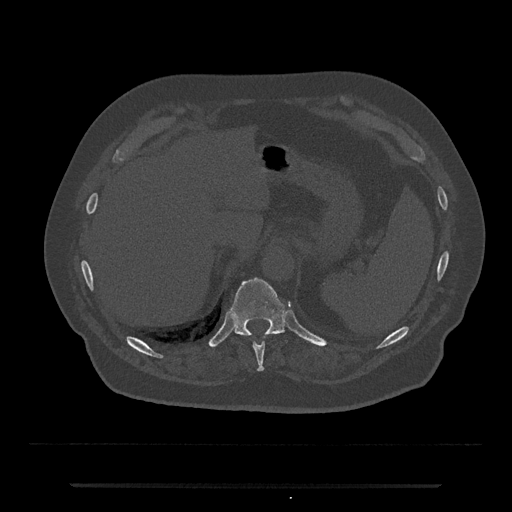
CT including the spine, one axial slice. Reconstruction kernel Br40s/3. 120 kVp. Bone window (W 1800 / L 400 HU). 0.5 mm slice thickness. 512 × 512 image matrix, field of view 434 × 434 mm. Male patient, age 80 years. From the clinical record (not read from this slice): primary cancer: prostate; vertebrae with lytic lesions (as recorded): L1, T11.
Structures marked on this image (semi-automatic segmentation, software-assisted and operator-edited):
- T10 vertebra: bounding box (x1, y1, x2, y2) in pixels: (253, 342, 265, 371)
- T11 vertebra: (230, 278, 288, 343)